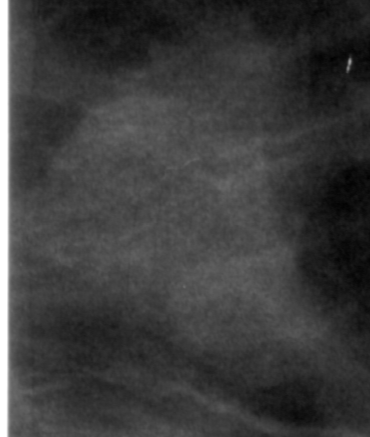
Region of interest cut from a scanned film mammogram (one marked finding), right breast, CC view, BI-RADS breast density category 1 (scale 1–4).
- Mass, shape lobulated, margins ill defined; BI-RADS assessment category 4; subtlety rating 4 on a 1 (subtle) to 5 (obvious) scale; pathology result (as recorded, not read from the image): benign.